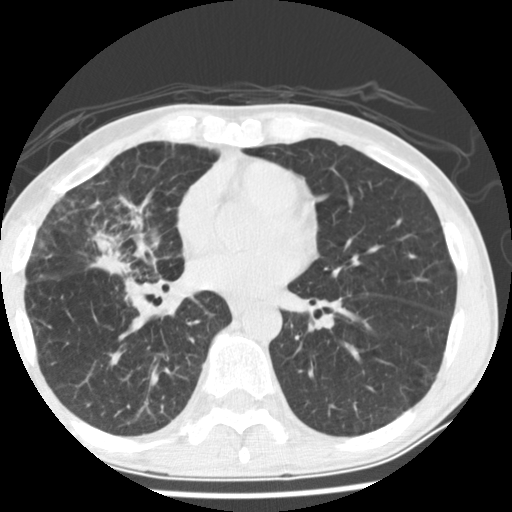
Low-dose screening chest CT, one axial slice. Position 75 of 162 along the scan axis. Reconstruction kernel STANDARD. 120 kVp. Lung window (W 1500 / L -600 HU). 2.5 mm slice thickness. 512 × 512 image matrix.
Structures marked on this image (outlined manually by an expert reader):
- lesion 1 (tumor, middle lobe of right lung): bounding box <77,231,116,276> (left, top, right, bottom; pixels)